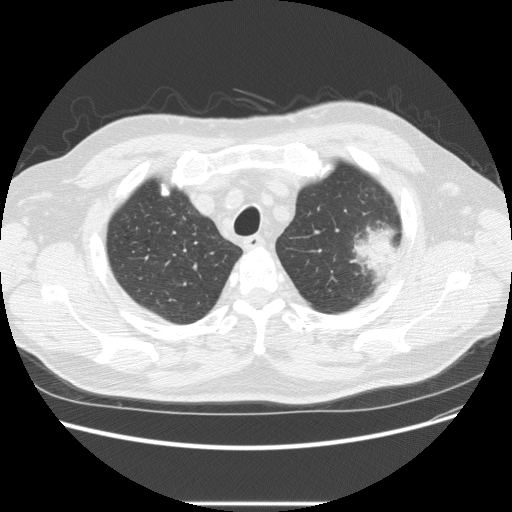
Low-dose screening chest CT, axial slice. Baseline annual screen. Lung window (W 1500 / L -600 HU). Standard (soft-tissue) reconstruction kernel (STANDARD). Male, age 73 years at enrolment. Former smoker at enrolment.
Expert-annotated lung lesion, bounding box [x1, y1, x2, y2] px = [332, 216, 408, 283]. The screening reader recorded 2 non-calcified nodules or masses ≥4 mm on this exam (left upper lobe, right upper lobe); which of them this box marks is not recorded. Official screen result: positive, change unspecified: nodule(s) >= 4 mm or enlarging nodule(s), mass(es), or other non-specific abnormalities suspicious for lung cancer. Lung cancer was diagnosed 11 days after this screen: bronchiolo-alveolar adenocarcinoma, NOS, other location, well differentiated (G1), stage IV (AJCC 6th edition).